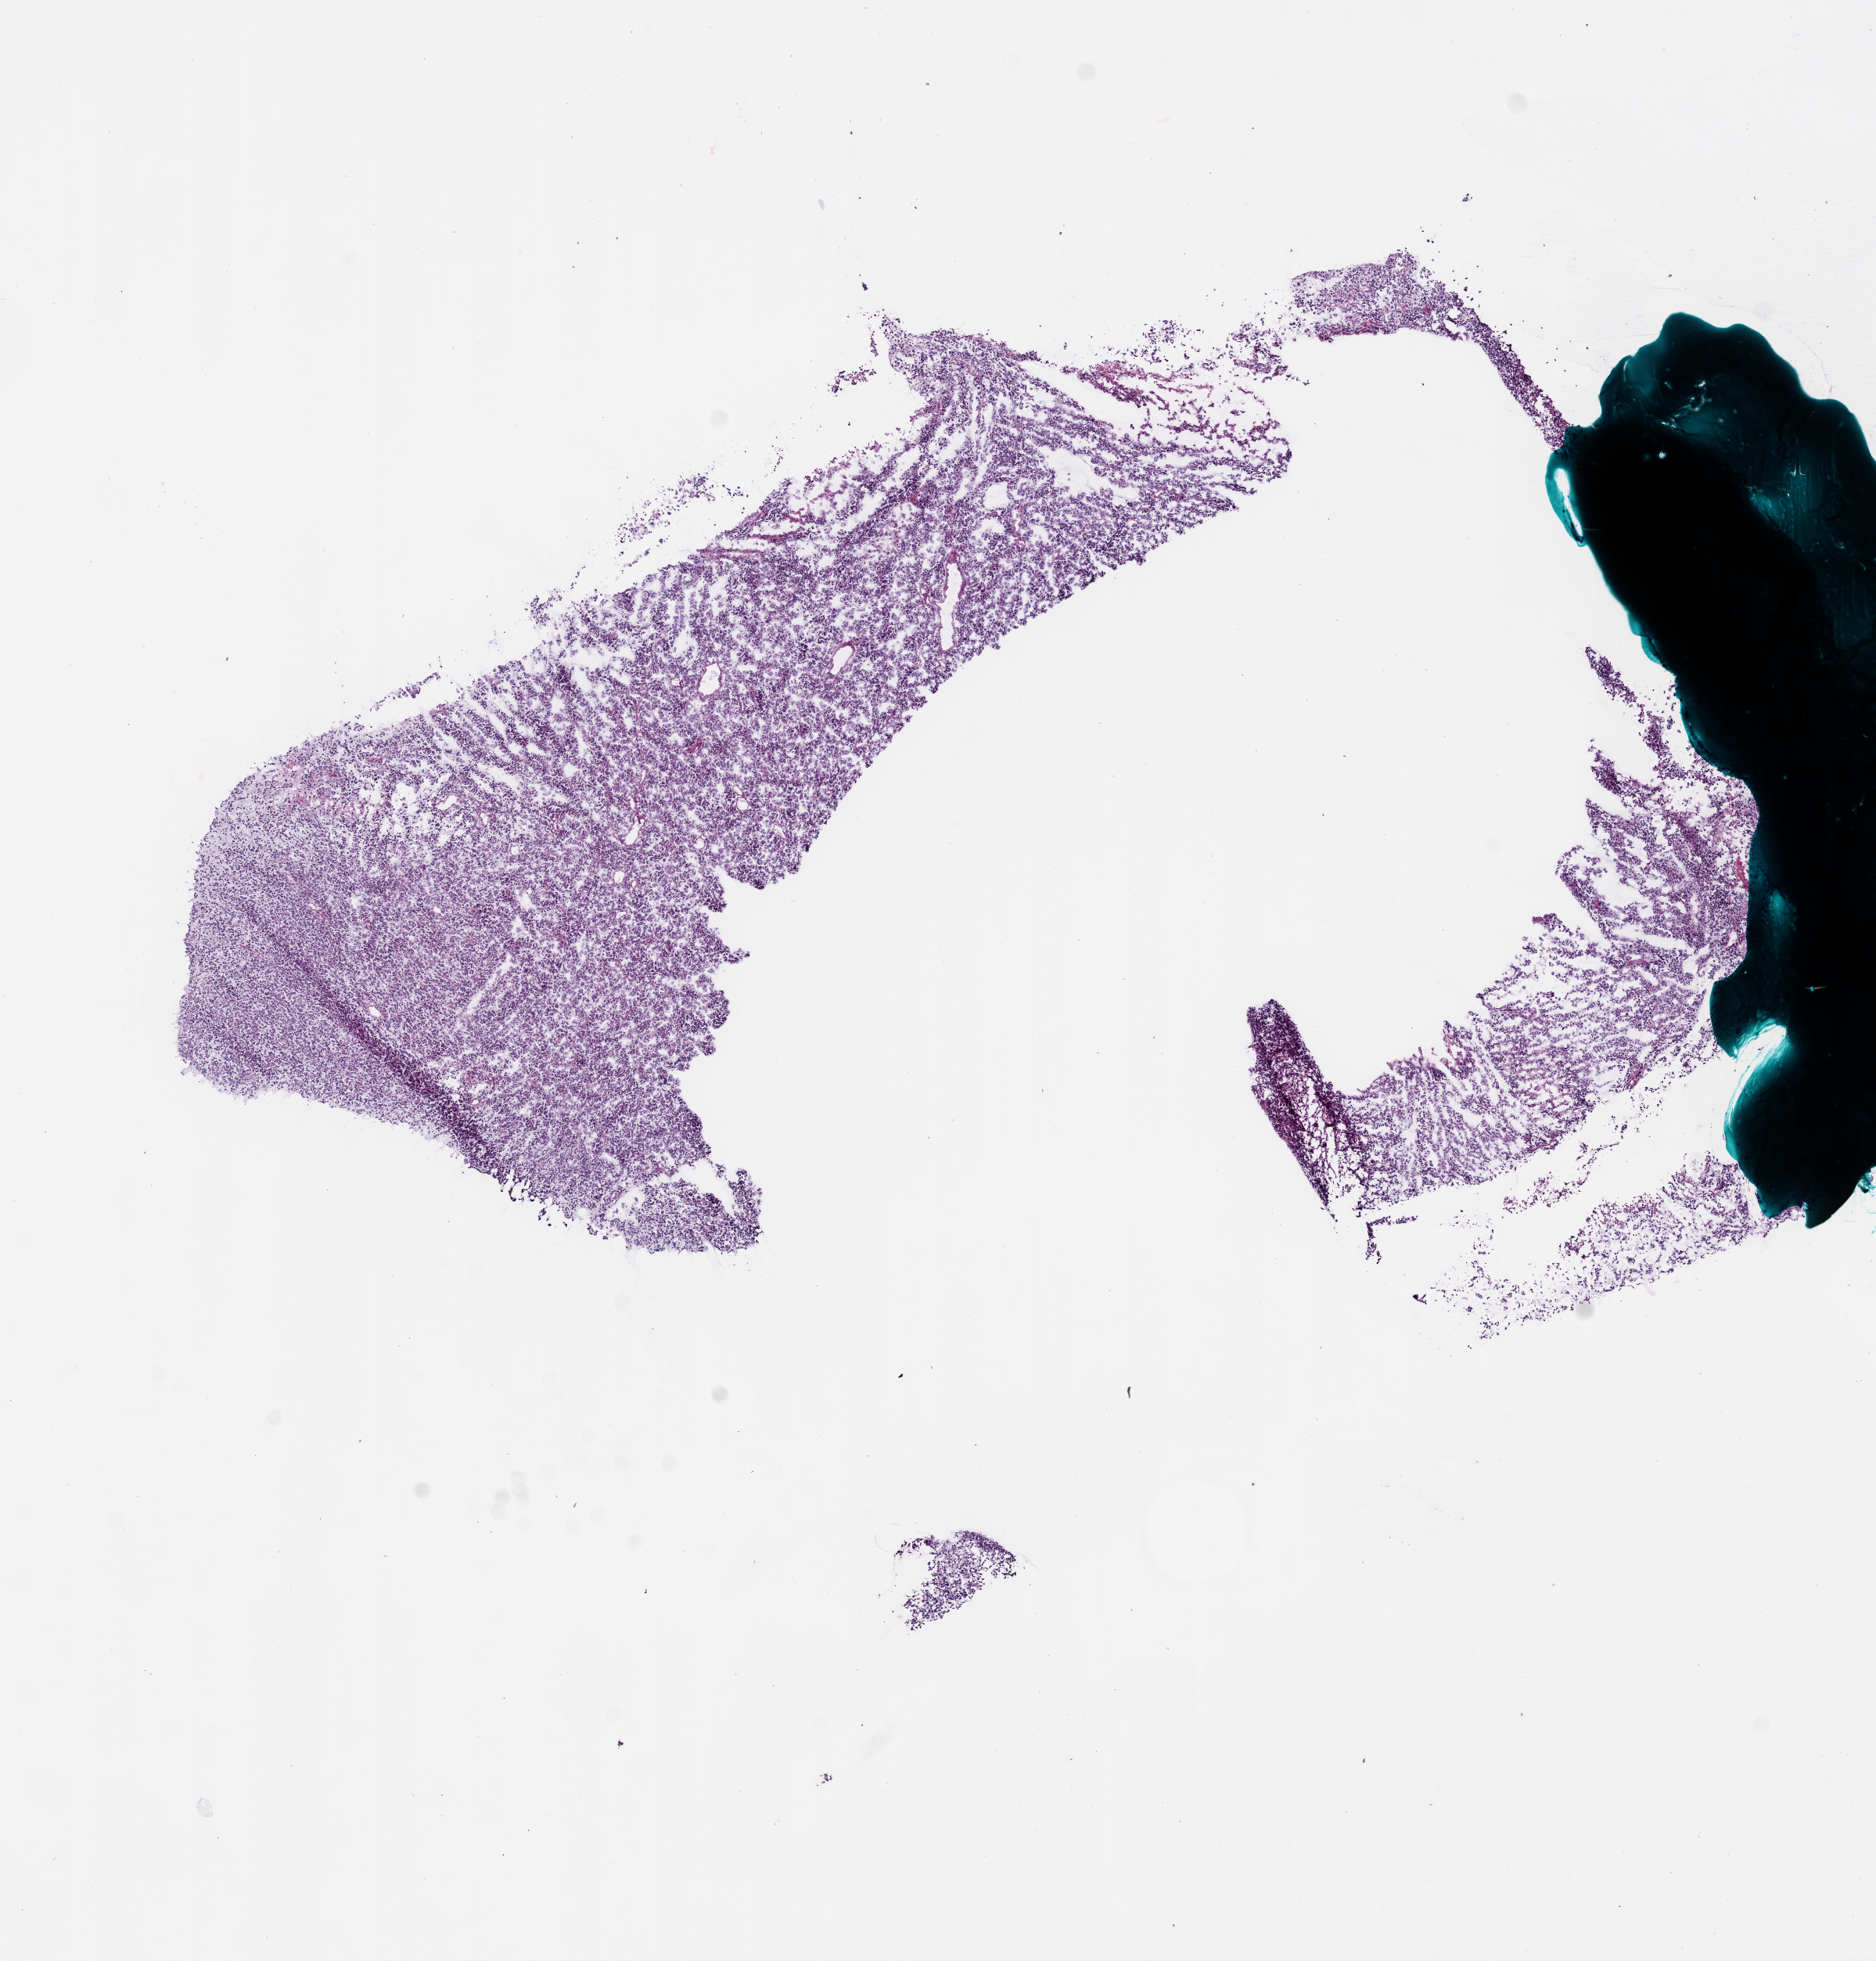
Digitized H&E tissue section (whole slide), a low-resolution overview of the entire scanned area, about 9.7 x 10.1 mm, frozen section from the bottom of the tissue portion, sample: primary tumour, brain. Patient: female, age at initial diagnosis 52 years. Composition of this section per pathologist review: tumour cells 95%, tumour nuclei 98%, stromal cells 3%, necrosis 2%.
Histologic diagnosis: Glioblastoma.